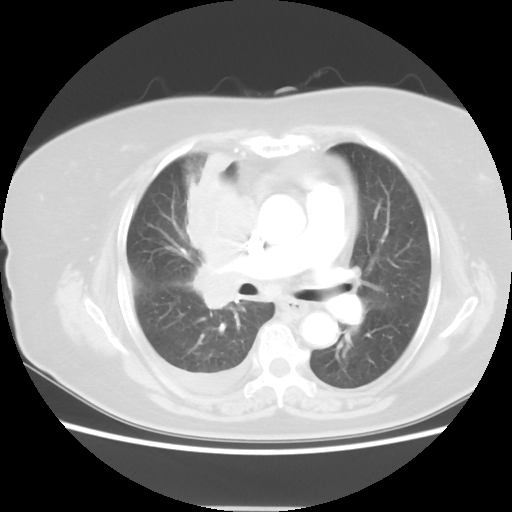
Chest CT, one axial slice; position 28 of 48 along the scan axis; 120 kVp; lung window (W 1500 / L -600 HU); 512 × 512 image matrix, field of view 360 × 360 mm. Female patient, age 73 years. From the clinical record (not read from this slice): clinical TNM (as recorded): T3 N3 M1b; histopathological grade: G3.
Annotated regions visible in this slice (rectangle marked by the reading radiologist):
- lung tumour (recorded histology: small cell carcinoma): bounding box <187,142,278,315> (left, top, right, bottom; pixels)